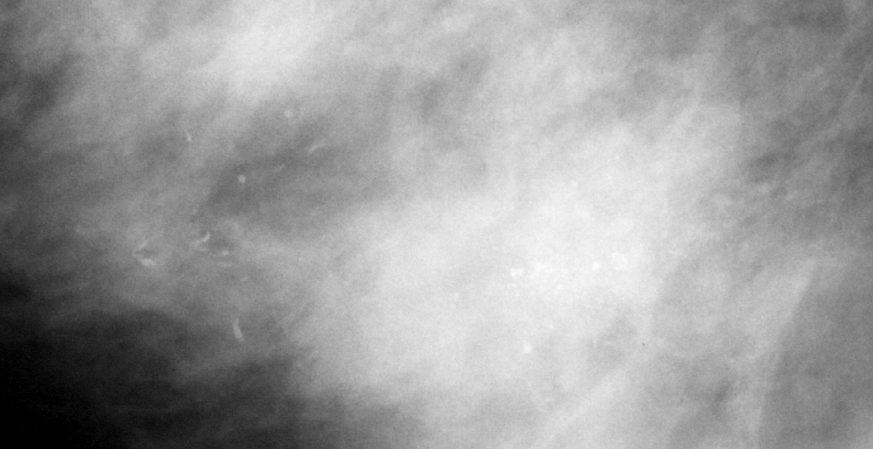
Cropped region of a digitized screen-film mammogram centred on a radiologist-marked abnormality; right breast; MLO view.
Finding: calcifications, morphology fine linear branching, distribution segmental; BI-RADS assessment category 5; subtlety rating 4 on a 1 (subtle) to 5 (obvious) scale; pathology result (as recorded, not read from the image): malignant.